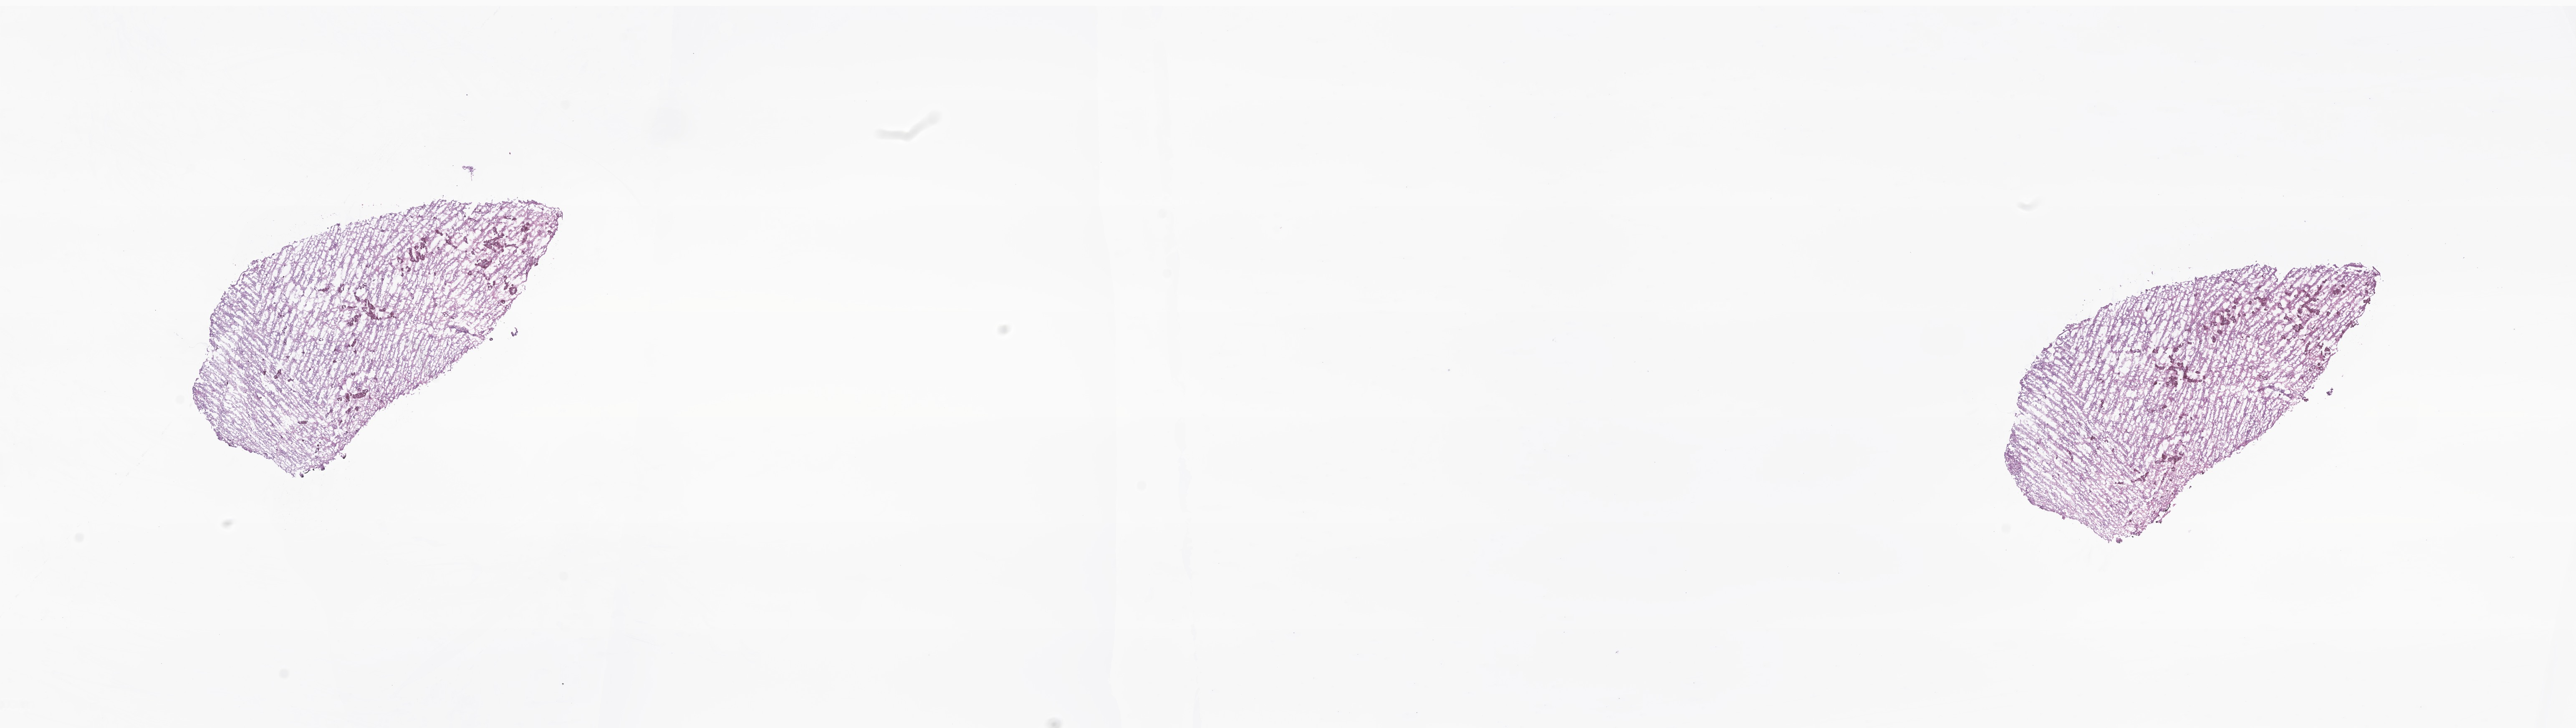
Whole-slide image, hematoxylin and eosin (H&E) stain of tumor tissue from the brain, shown as a low-resolution overview of the whole scanned area (about 26.0 x 7.4 mm). Frozen section (OCT-embedded). Female patient, age 100 months (8 years 4 months).
Diagnosis (ICD-O-3 morphology term): Neoplasm, malignant.